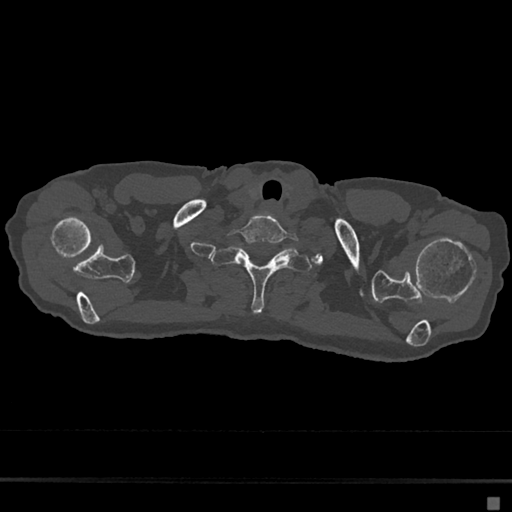
CT including the spine, one axial slice; position 620 of 797 along the scan axis; 120 kVp; bone window (W 1800 / L 400 HU); 0.5 mm slice thickness; 512 × 512 image matrix, field of view 360 × 360 mm. Patient: female, 68 years. Case-level facts recorded for this patient, not image findings: primary cancer: renal.
Annotated regions visible in this slice (semi-automatic segmentation, software-assisted and operator-edited):
- T1 vertebra: bounding box <211,247,312,313> (left, top, right, bottom; pixels)